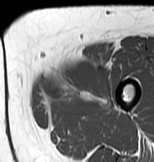
MRI of an extremity soft-tissue mass, one axial slice; position 17 of 83 along the scan axis; MR volume resampled by the dataset authors to the PET/CT grid (not the native acquisition matrix); 154 × 162 image matrix, field of view 150 × 158 mm. Female patient. From the clinical record (not read from this slice): histological type: myxofibrosarcoma; grade: intermediate; site of the primary tumour: left thigh.
Structures marked on this image (expert contour drawn on MRI and transferred to this co-registered scan by the dataset authors):
- gross tumour volume including surrounding oedema: bounding box [x1, y1, x2, y2] px = [35, 61, 111, 113]
- gross tumour volume (mass): [42, 61, 104, 112]